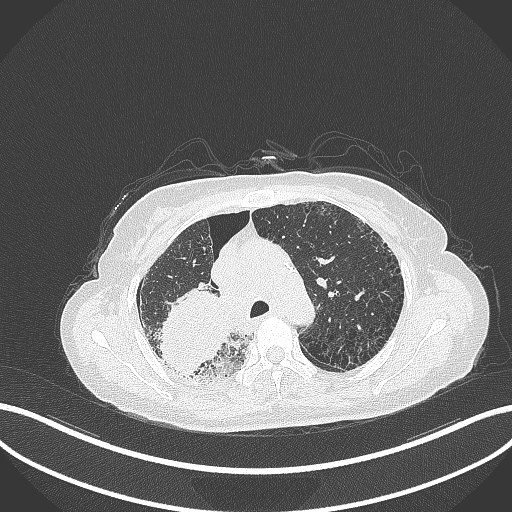
Chest CT, one axial slice. Slice 248 of 408 in the series (ordered by position). Reconstruction kernel B70f. Lung window (W 1500 / L -600 HU). 1 mm slice thickness. 512 × 512 image matrix, field of view 400 × 400 mm. Female patient, age 64 years. From the clinical record (not read from this slice): clinical TNM (as recorded): T3 N3 M0.
Annotated regions visible in this slice (bounding box drawn by a radiologist):
- lung tumour (recorded histology: squamous cell carcinoma): bounding box (x1, y1, x2, y2) in pixels: (154, 286, 233, 375)